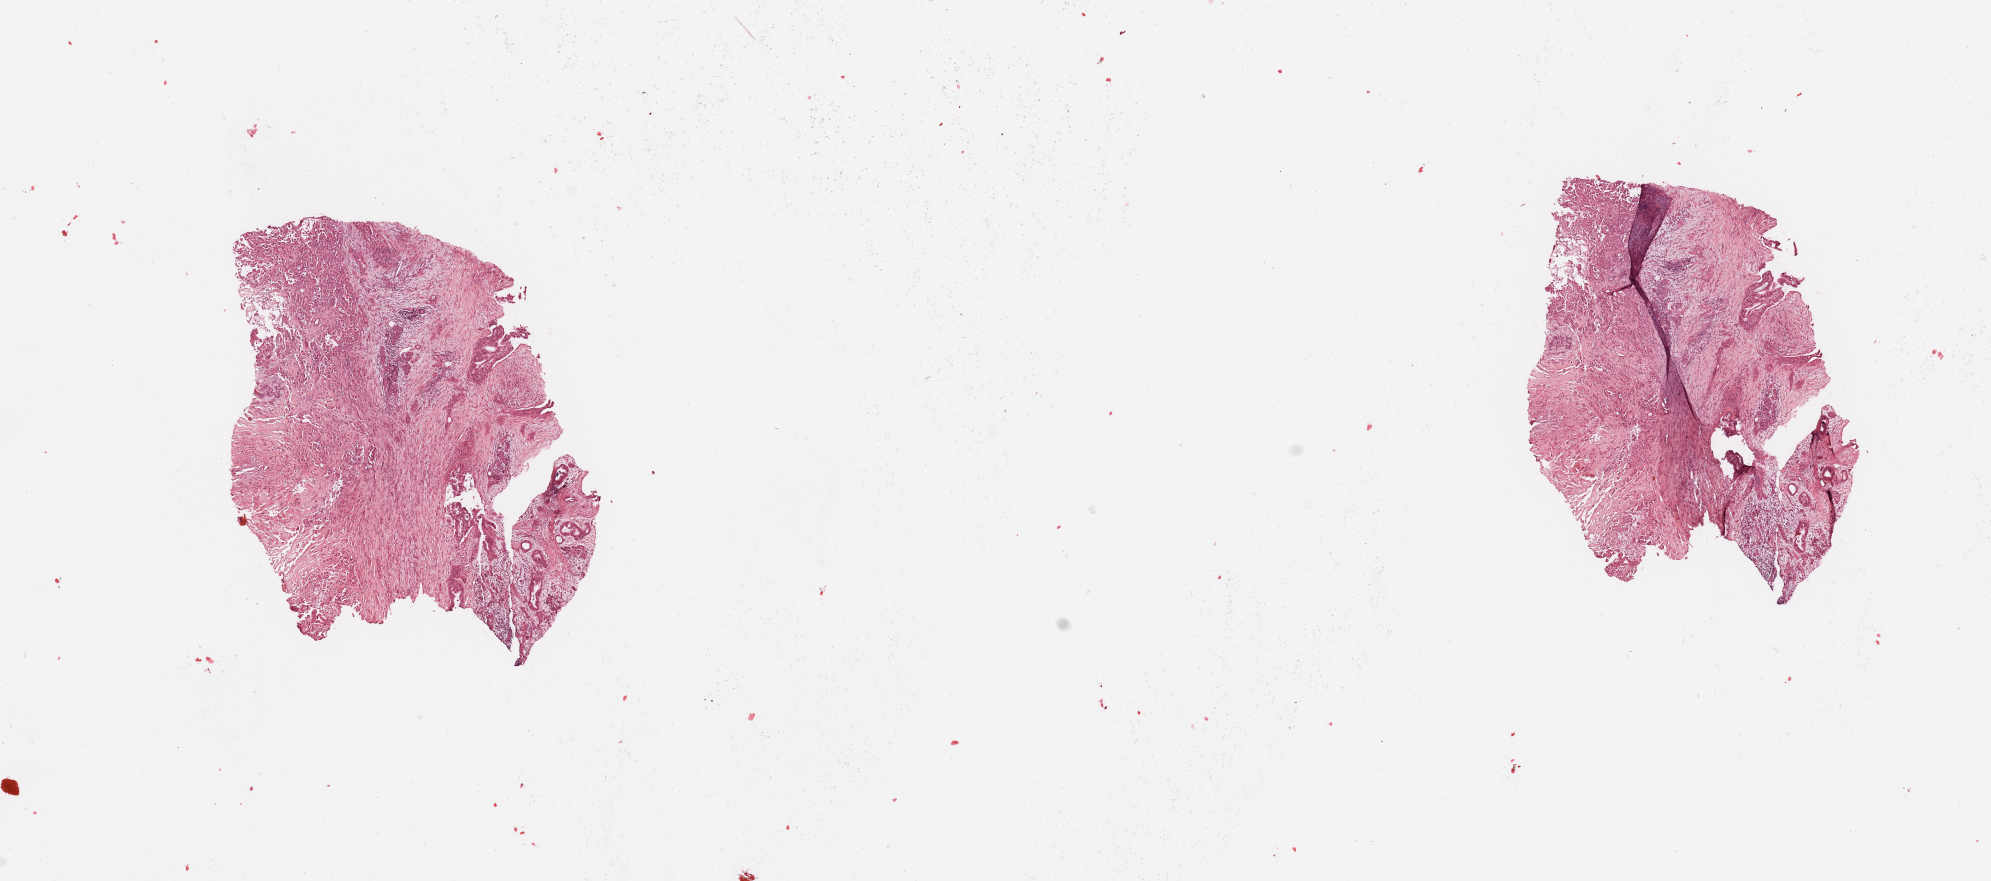
Whole-slide histology image, H&E-stained, shown as a low-resolution overview of the whole scanned area (about 15.8 x 7.0 mm). Tumour tissue sample, sampled site: pancreas. Patient: male, age 68 years. Slide review estimates, as recorded: tumour nuclei 40%, necrosis 2%.
Diagnosis: Infiltrating duct carcinoma, NOS.